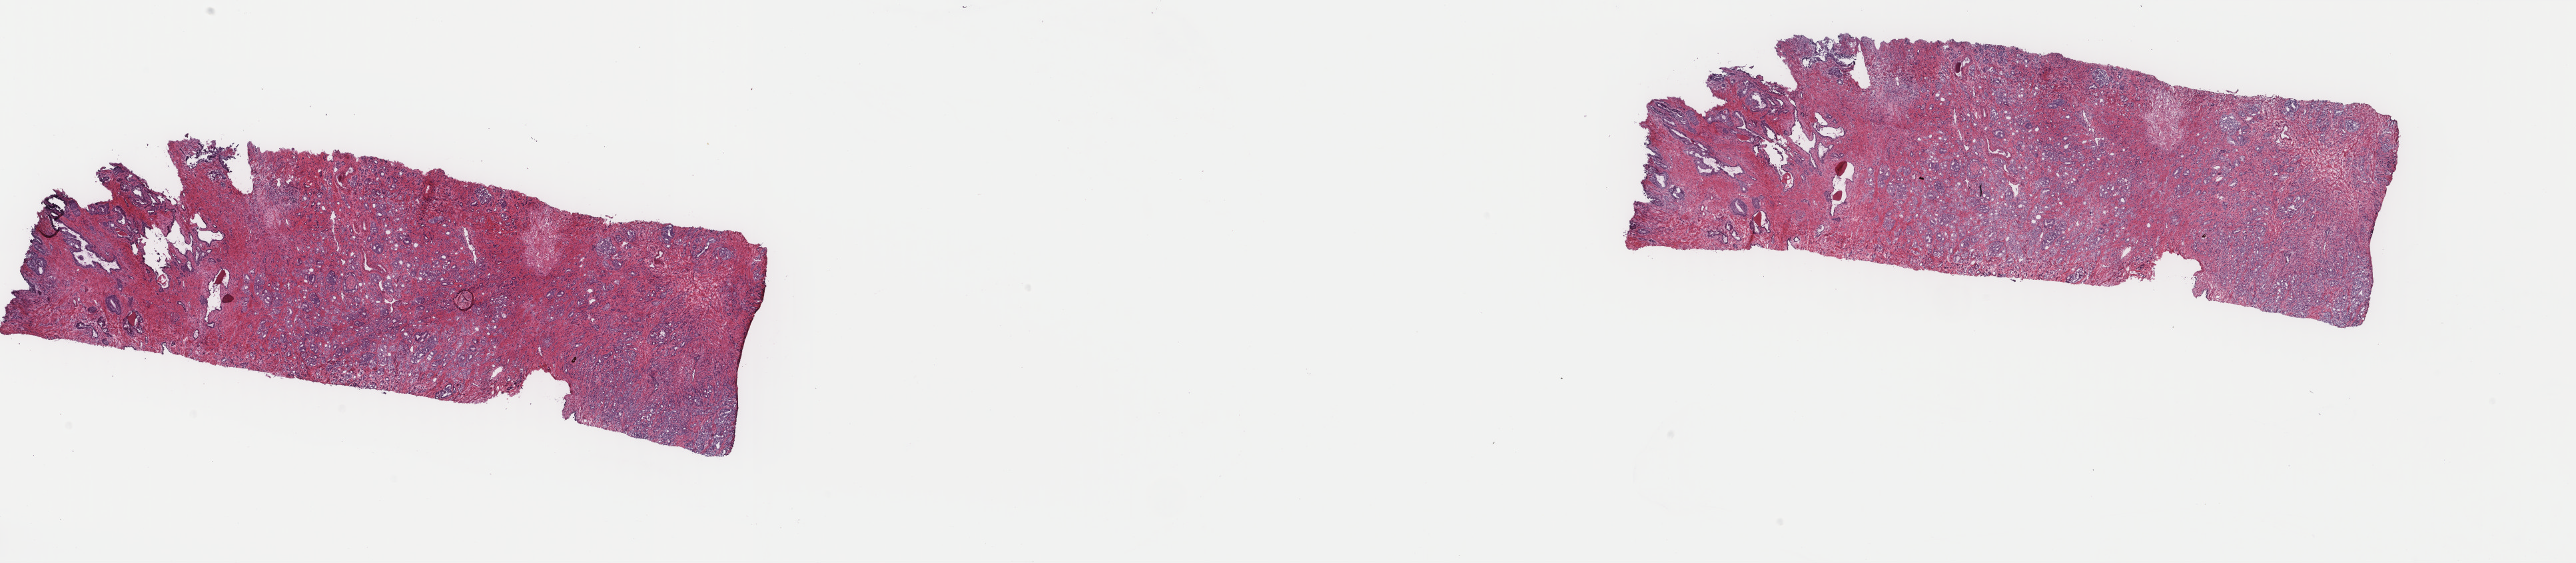
Digitized H&E-stained tissue section (whole slide) — a low-resolution overview of the entire scanned area, about 30.7 x 6.7 mm (slide scanned at 40x); frozen section from the top of the tissue portion; prostate, primary tumour sample. Male patient; age at initial diagnosis 59 years.
Pathologic diagnosis: Adenocarcinoma with mixed subtypes (prostate gland).